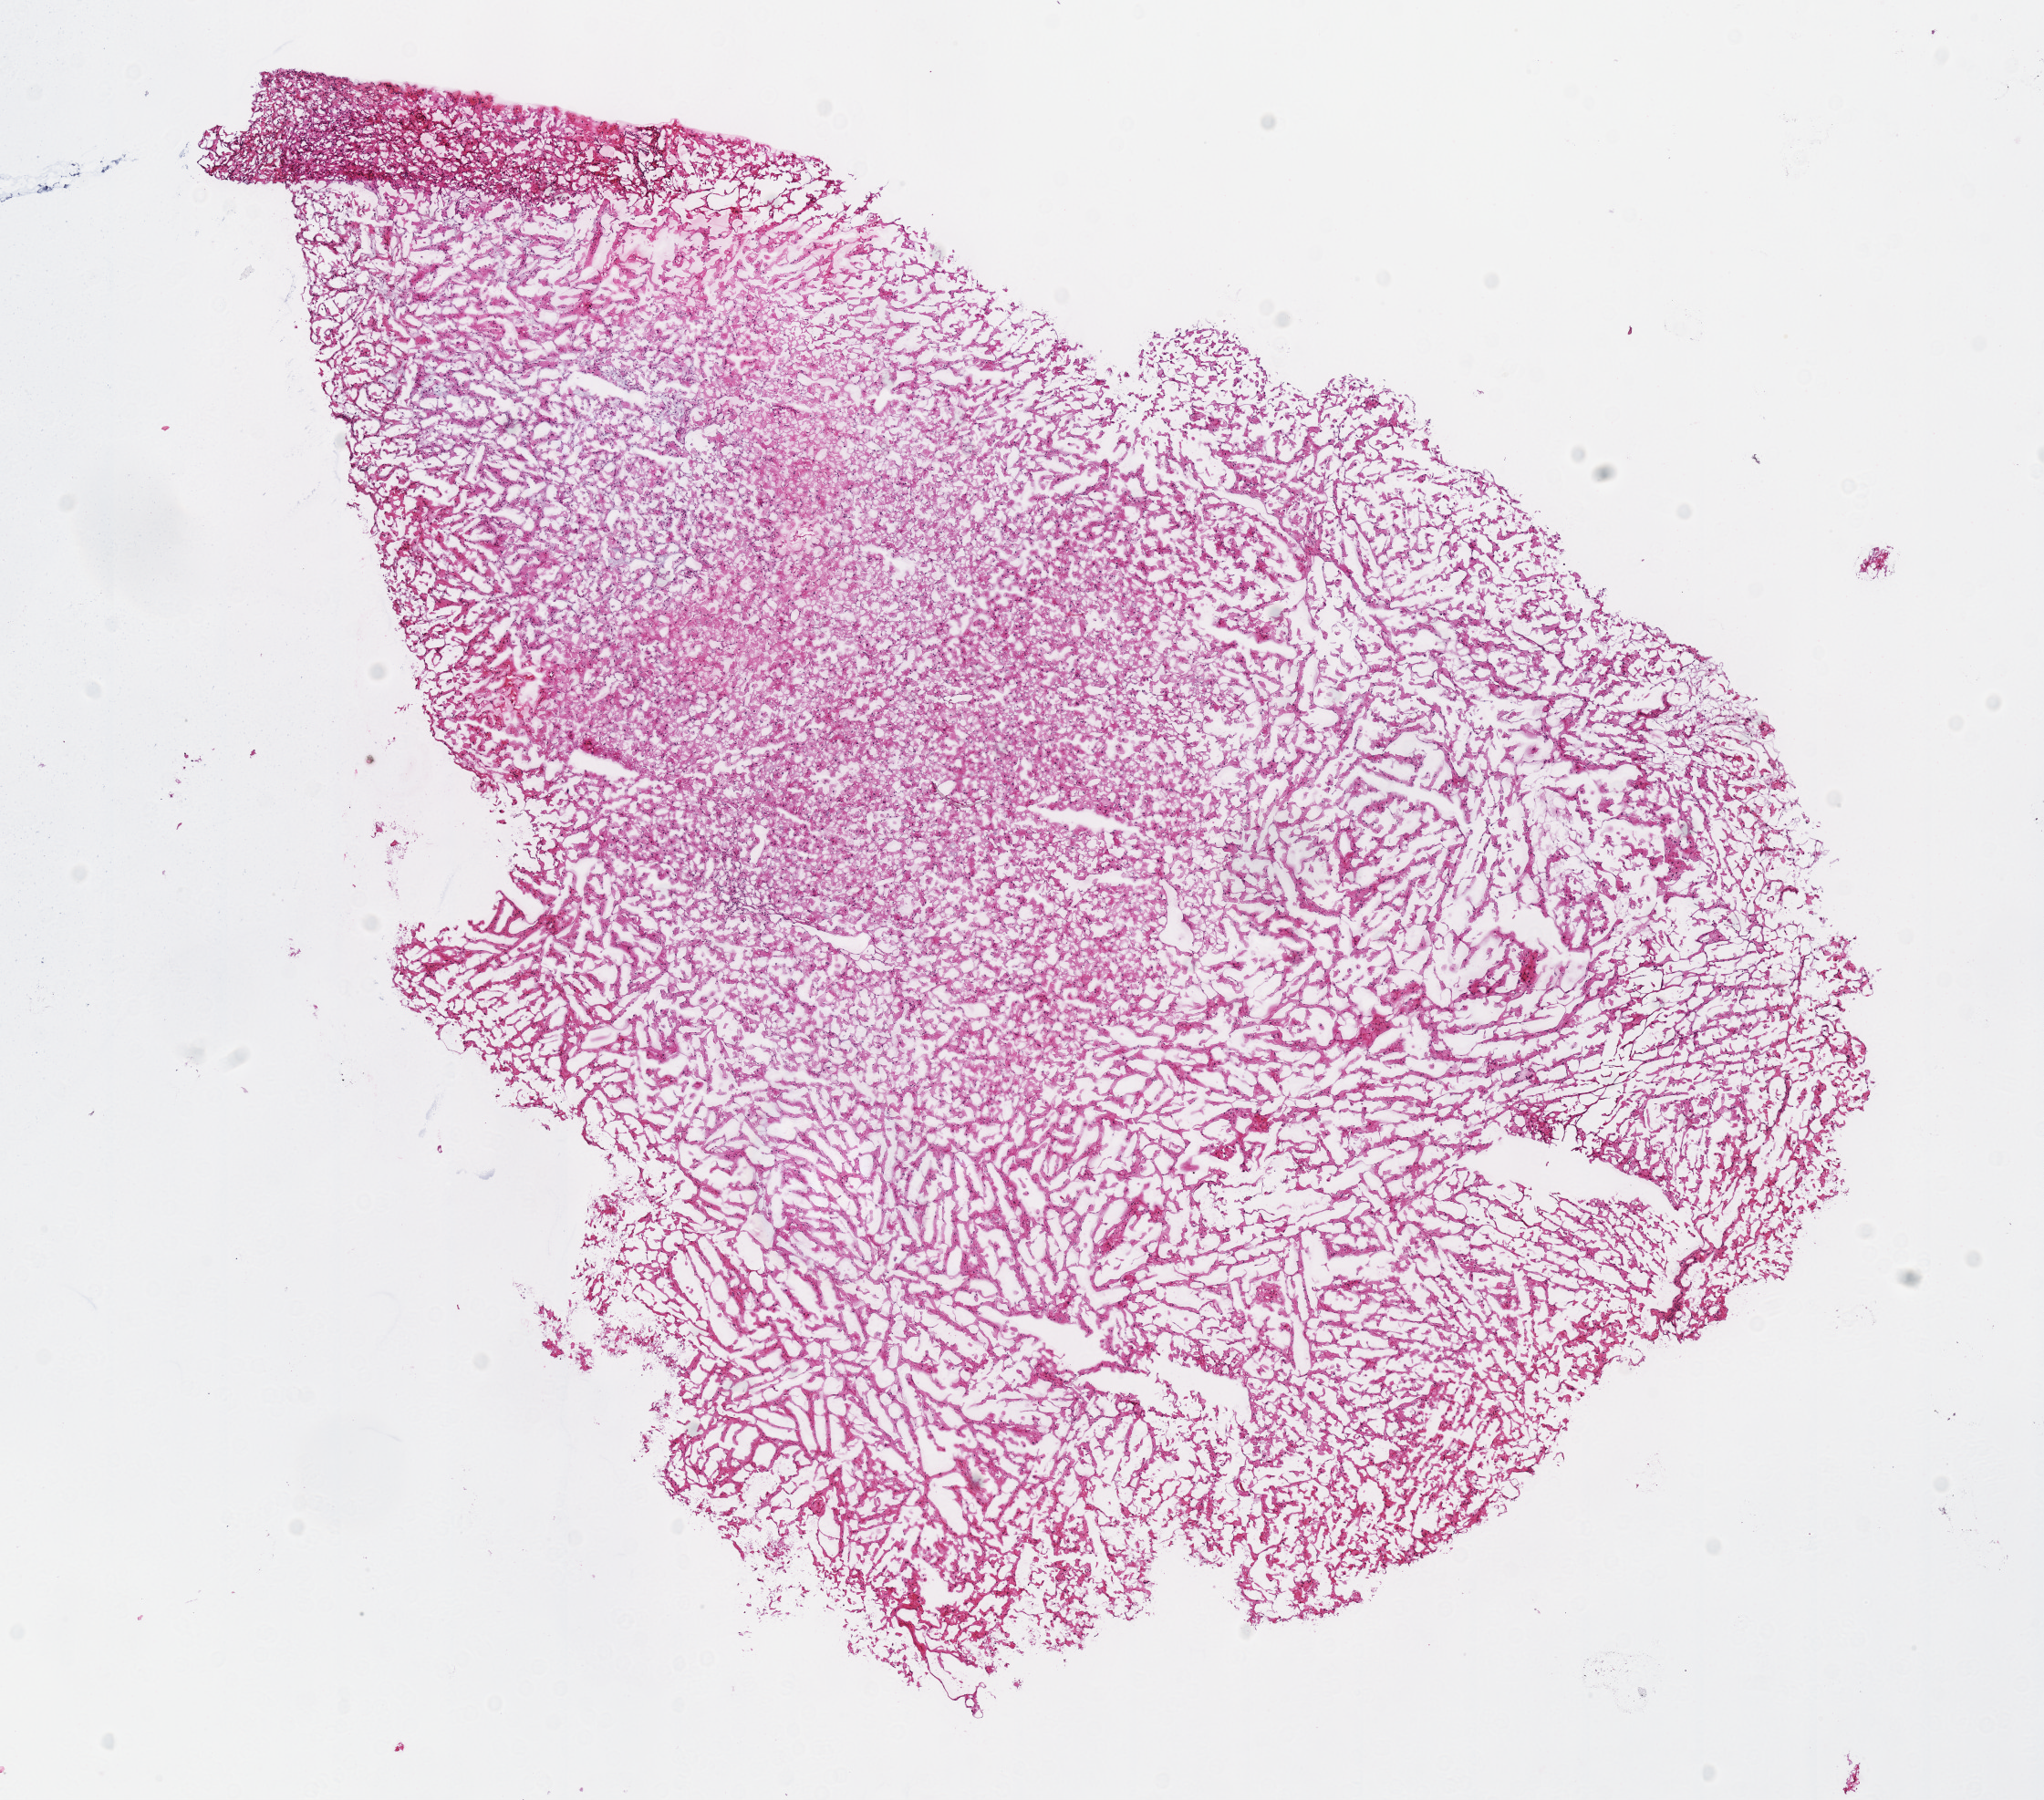
Whole-slide histology image, Hematoxylin and eosin (H&E) stained — low-resolution overview of the scanned area, about 8.8 x 7.8 mm. Frozen section. Sample: primary tumour, kidney. Male patient; age at initial diagnosis 29 years. Composition of this section per pathologist review: tumour cells 90%, tumour nuclei 85%, normal cells 0%, stromal cells 10%, necrosis 0%.
AJCC pathologic stage: III (7th edition). Histologic diagnosis: Renal cell carcinoma, chromophobe type.